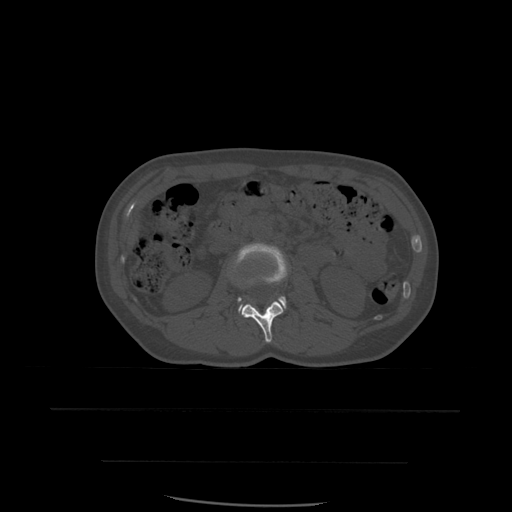
CT including the spine, one axial slice; slice 213 of 574 in the series (ordered by position); bone window (W 1800 / L 400 HU); 512 × 512 image matrix. Patient age 48 years. Case-level facts recorded for this patient, not image findings: primary cancer: lung.
Outlined on this slice (semi-automatic segmentation, software-assisted and operator-edited):
- L2 vertebra: bounding box (x1, y1, x2, y2) in pixels: (240, 302, 284, 343)
- L3 vertebra: (234, 243, 288, 312)